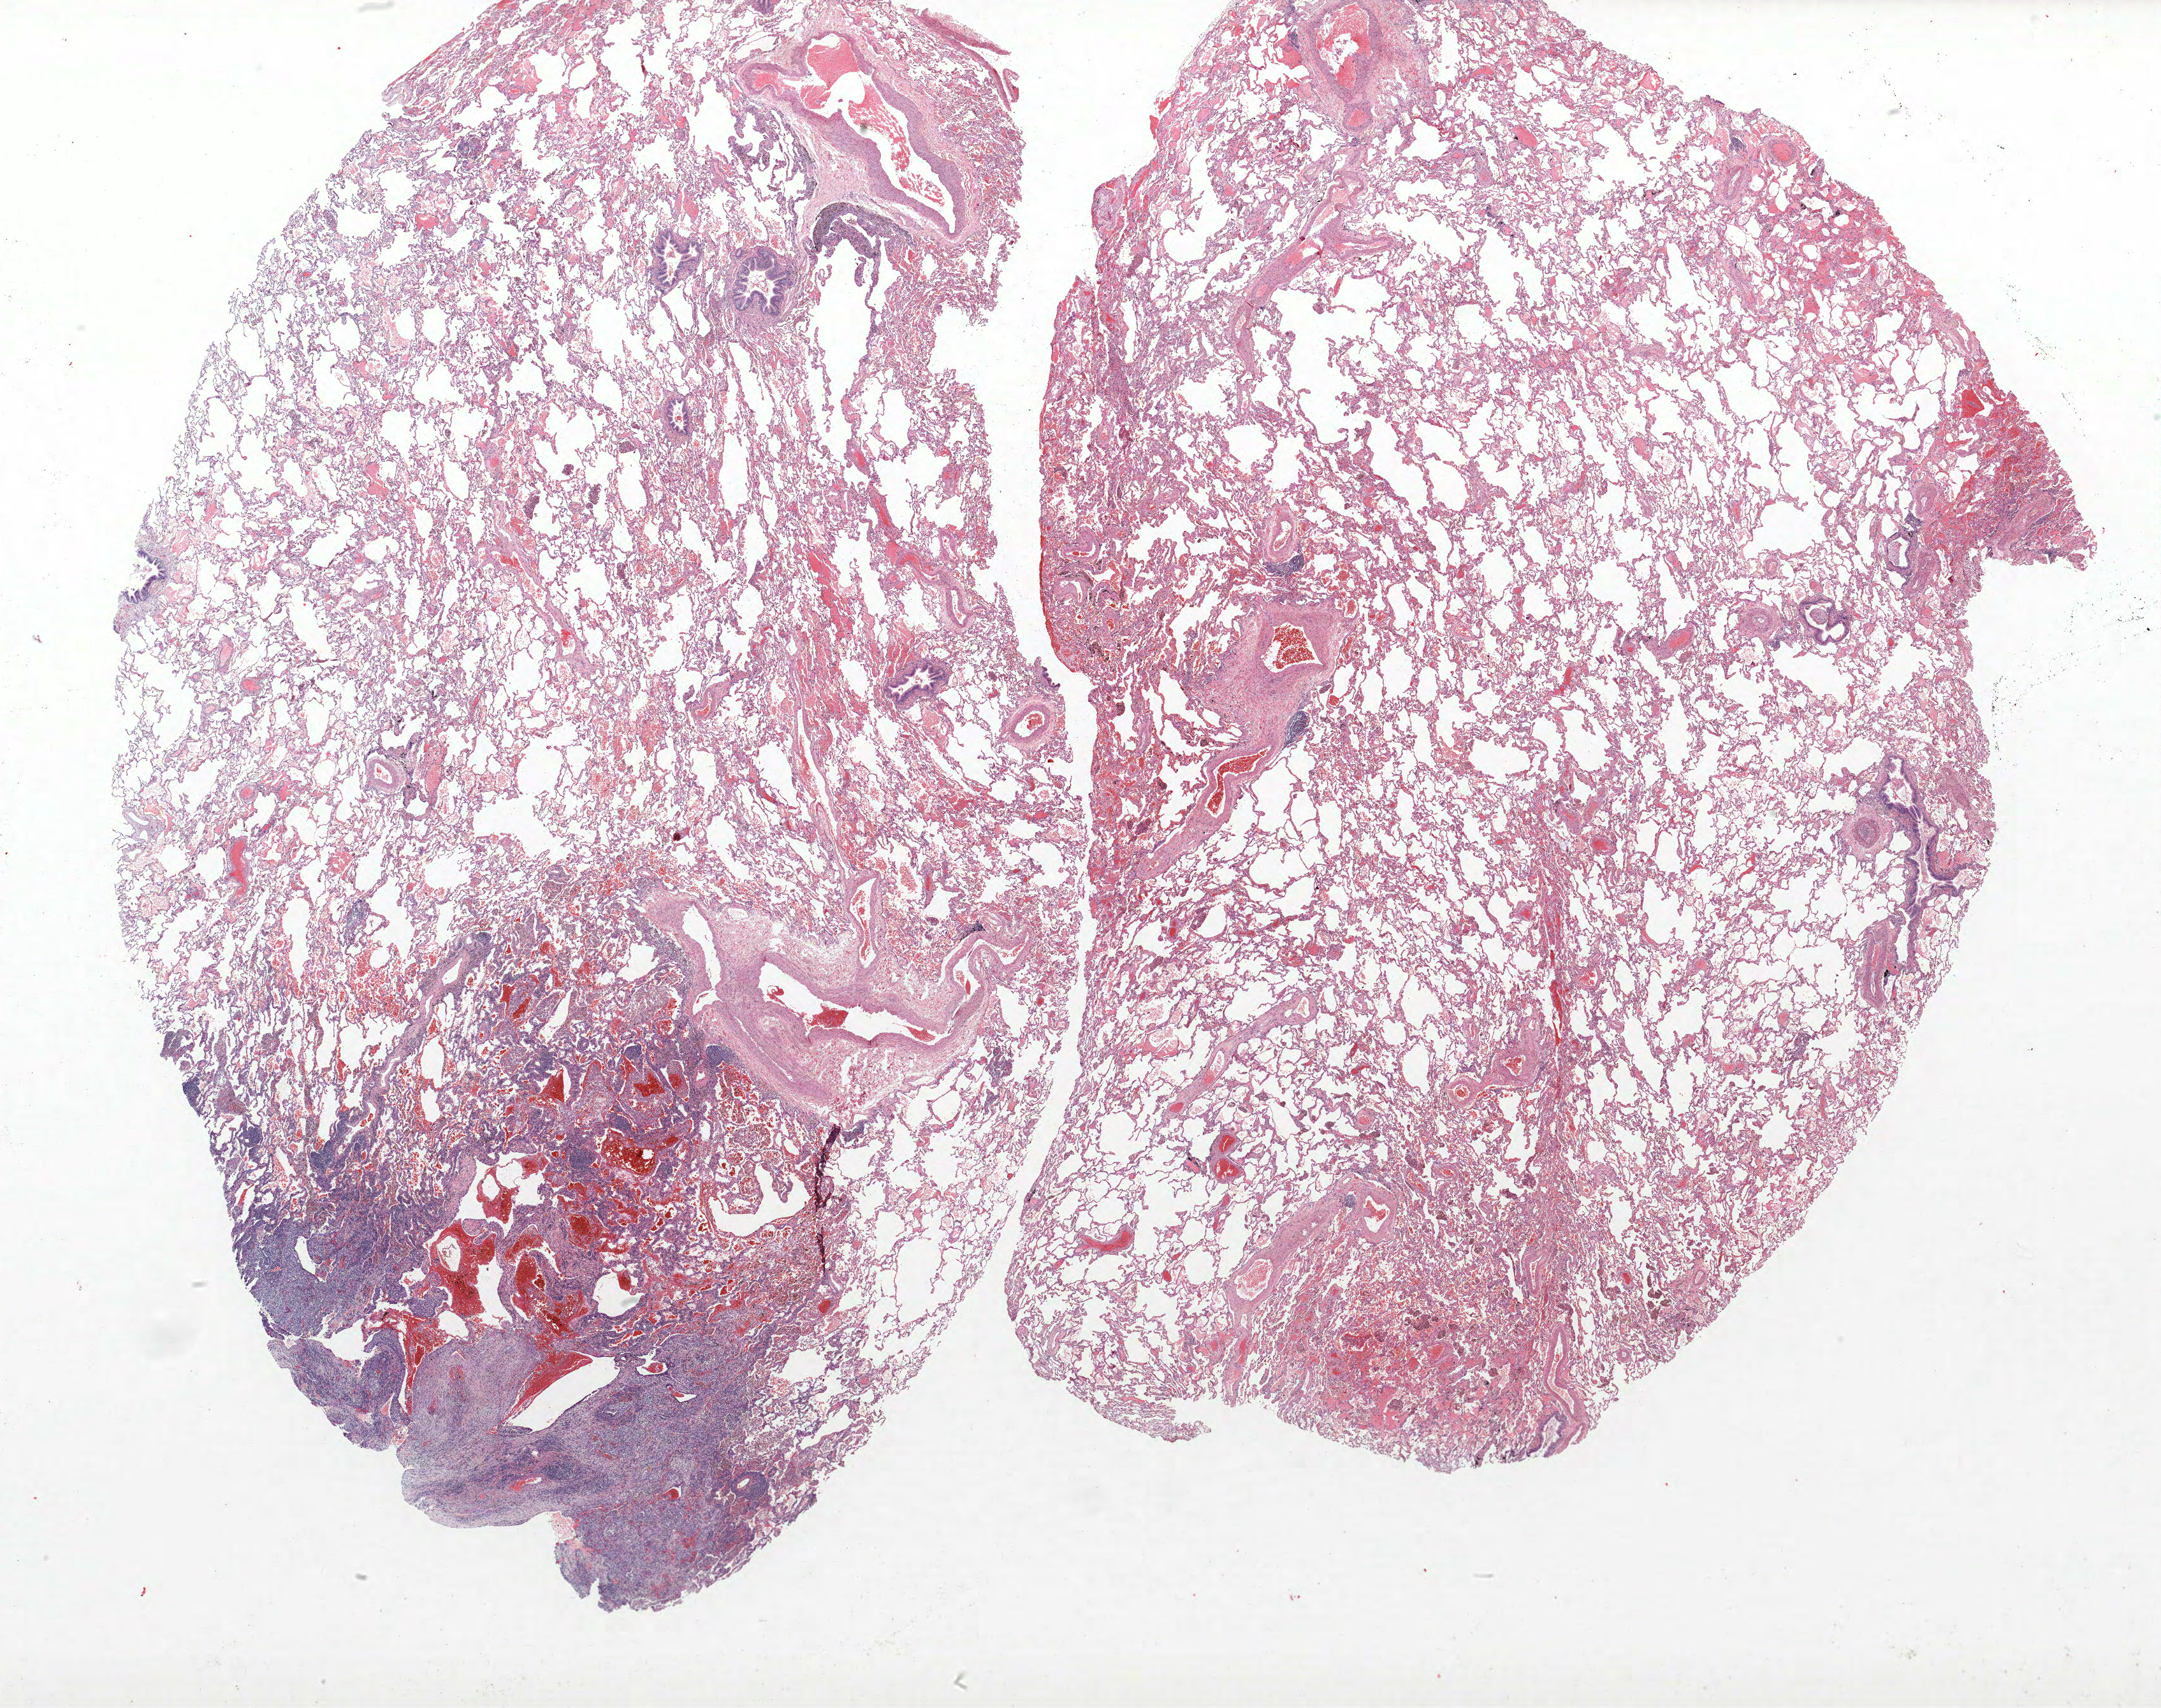
Hematoxylin and eosin (H&E) stained whole-slide image, shown as a low-resolution overview of the whole scanned area (about 27.1 x 21.4 mm); formalin-fixed paraffin-embedded (FFPE) section; lung. Male patient, aged 57 at enrolment. Current smoker at enrolment. Grade: moderately differentiated (G2).
Participant's lung-cancer diagnosis: Squamous cell carcinoma, NOS (ICD-O-3 8070/3). Primary tumour location (clinical record): left lower lobe. Stage (AJCC 6th edition): IA. Tumour size (pathology): 22 mm.